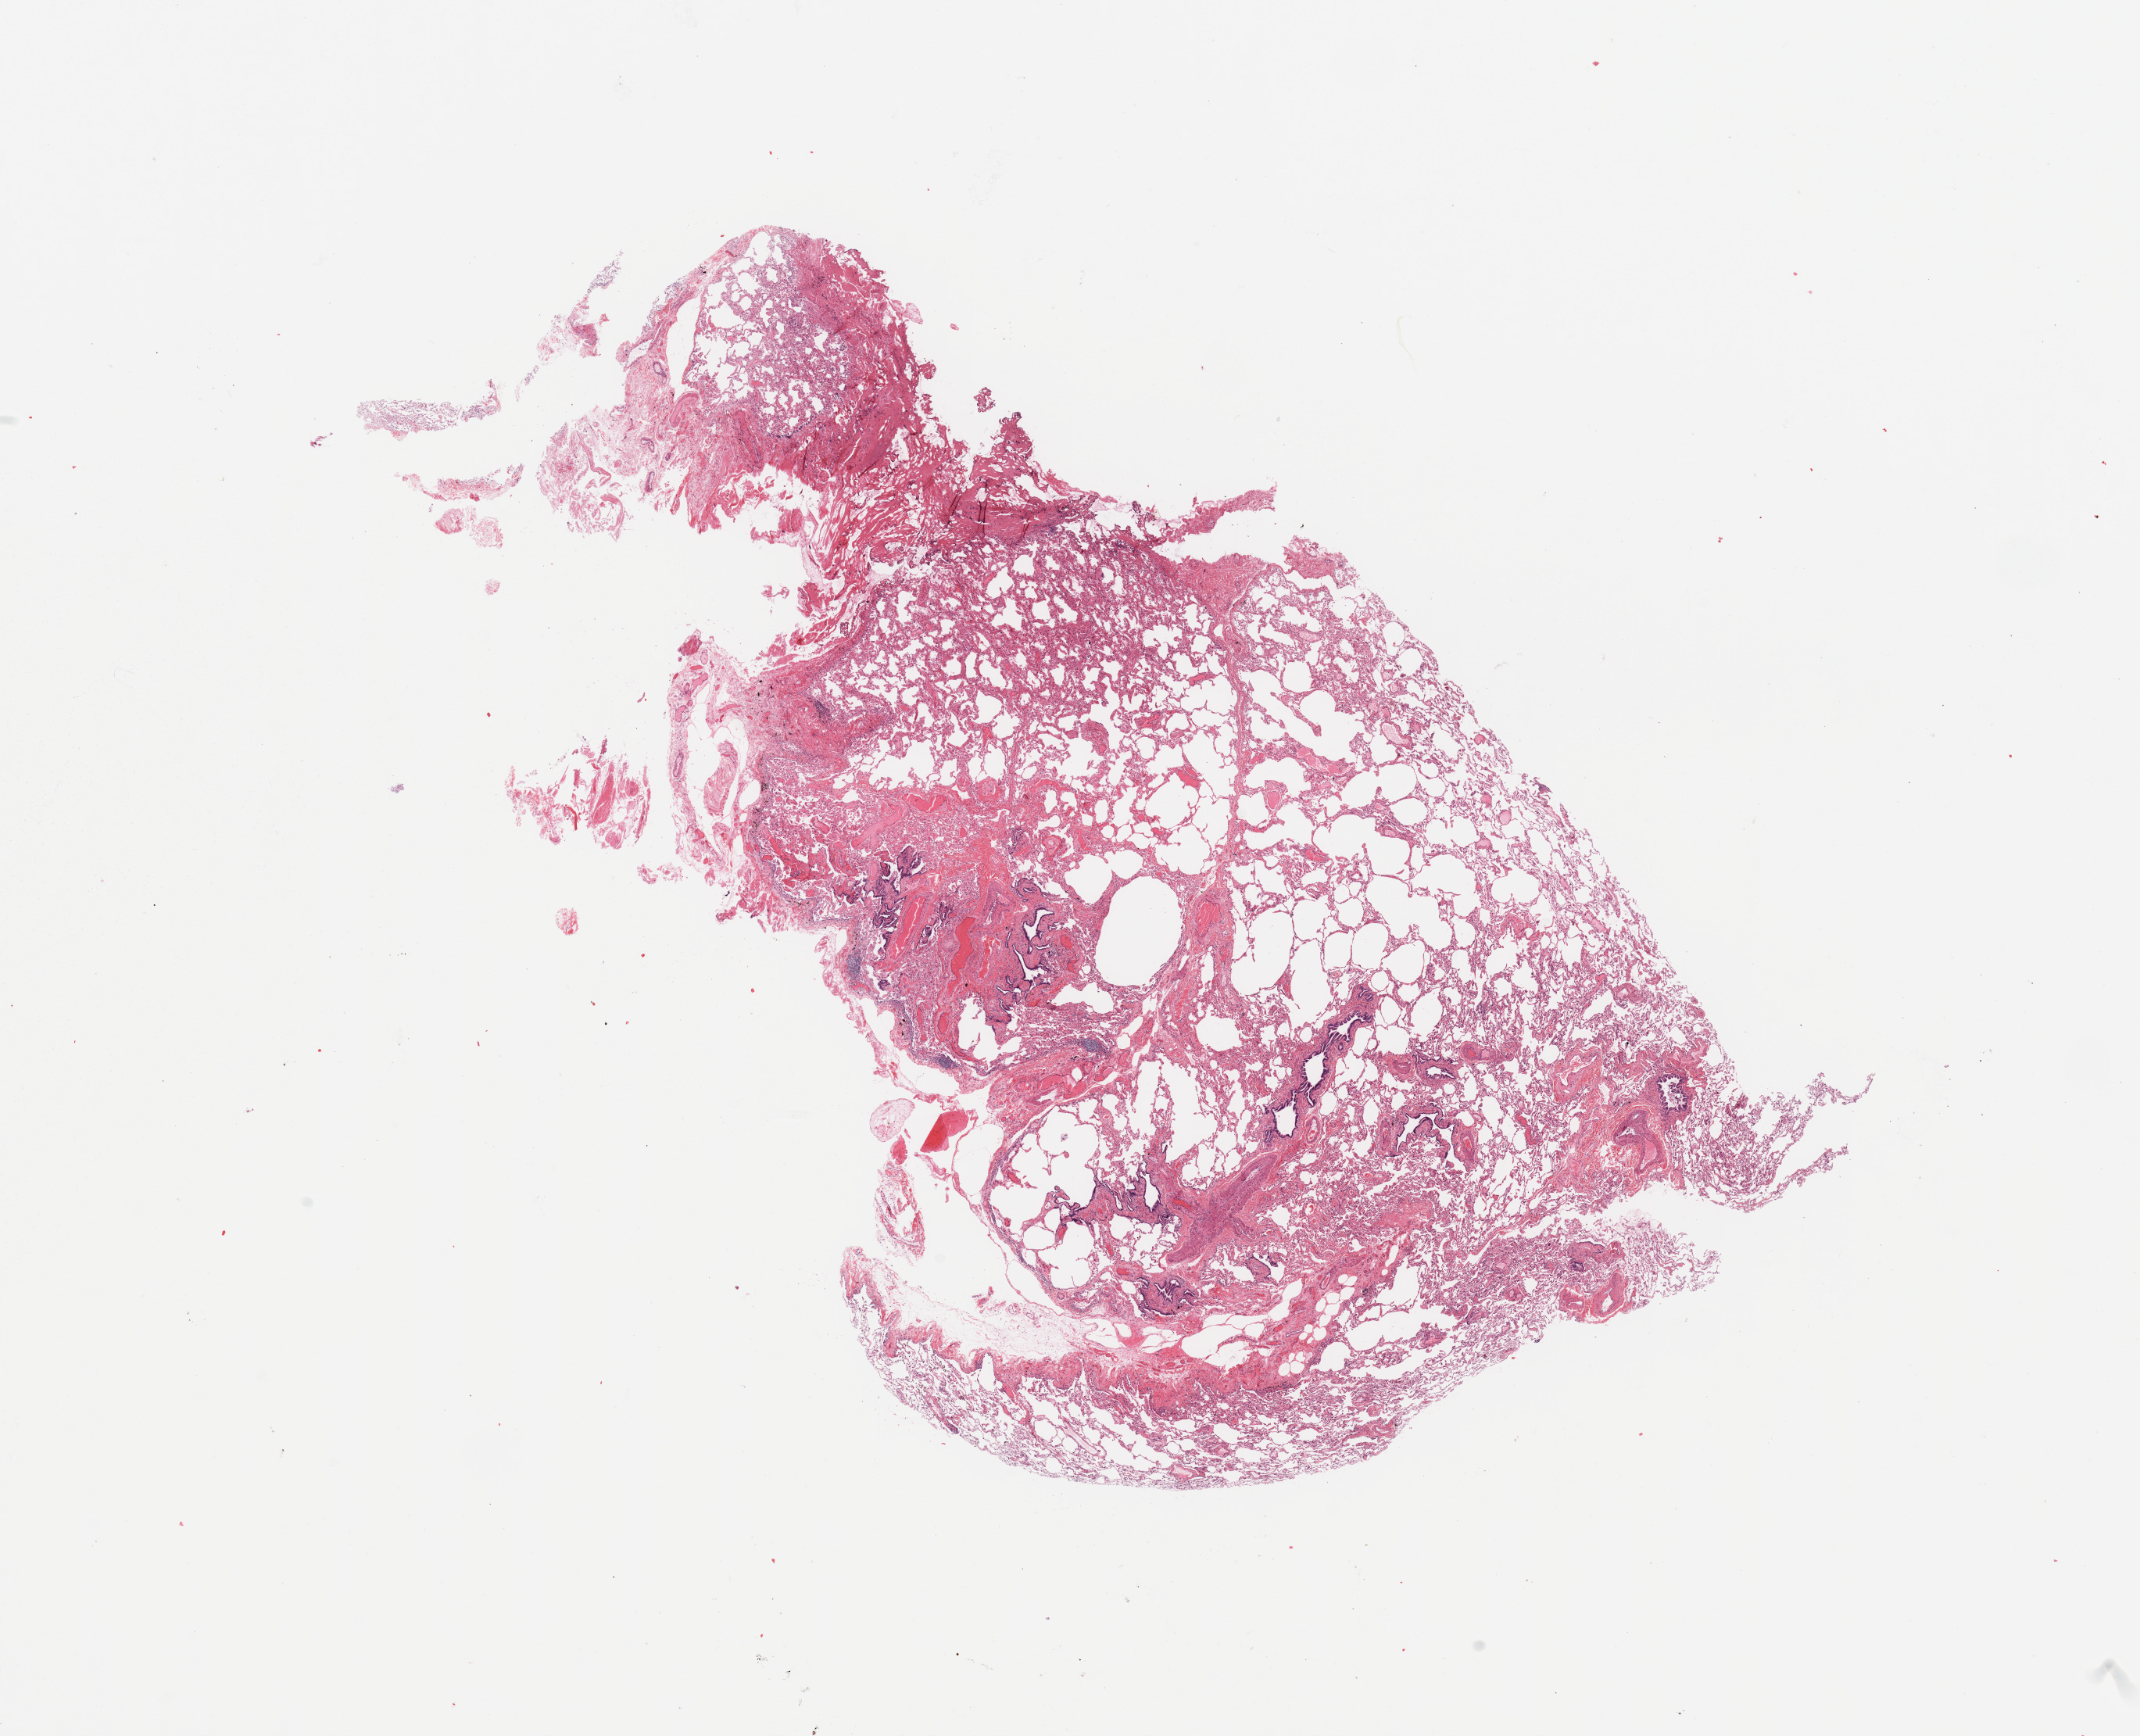
Whole-slide histology image, H&E-stained, shown as a low-resolution overview of the whole scanned area (about 21.7 x 17.6 mm). Normal (non-tumour) tissue sample, sampled site: lung. Patient: male, age 68 years.
This section: normal (non-tumour) tissue from the same patient. Patient diagnosis: Squamous cell carcinoma, NOS.